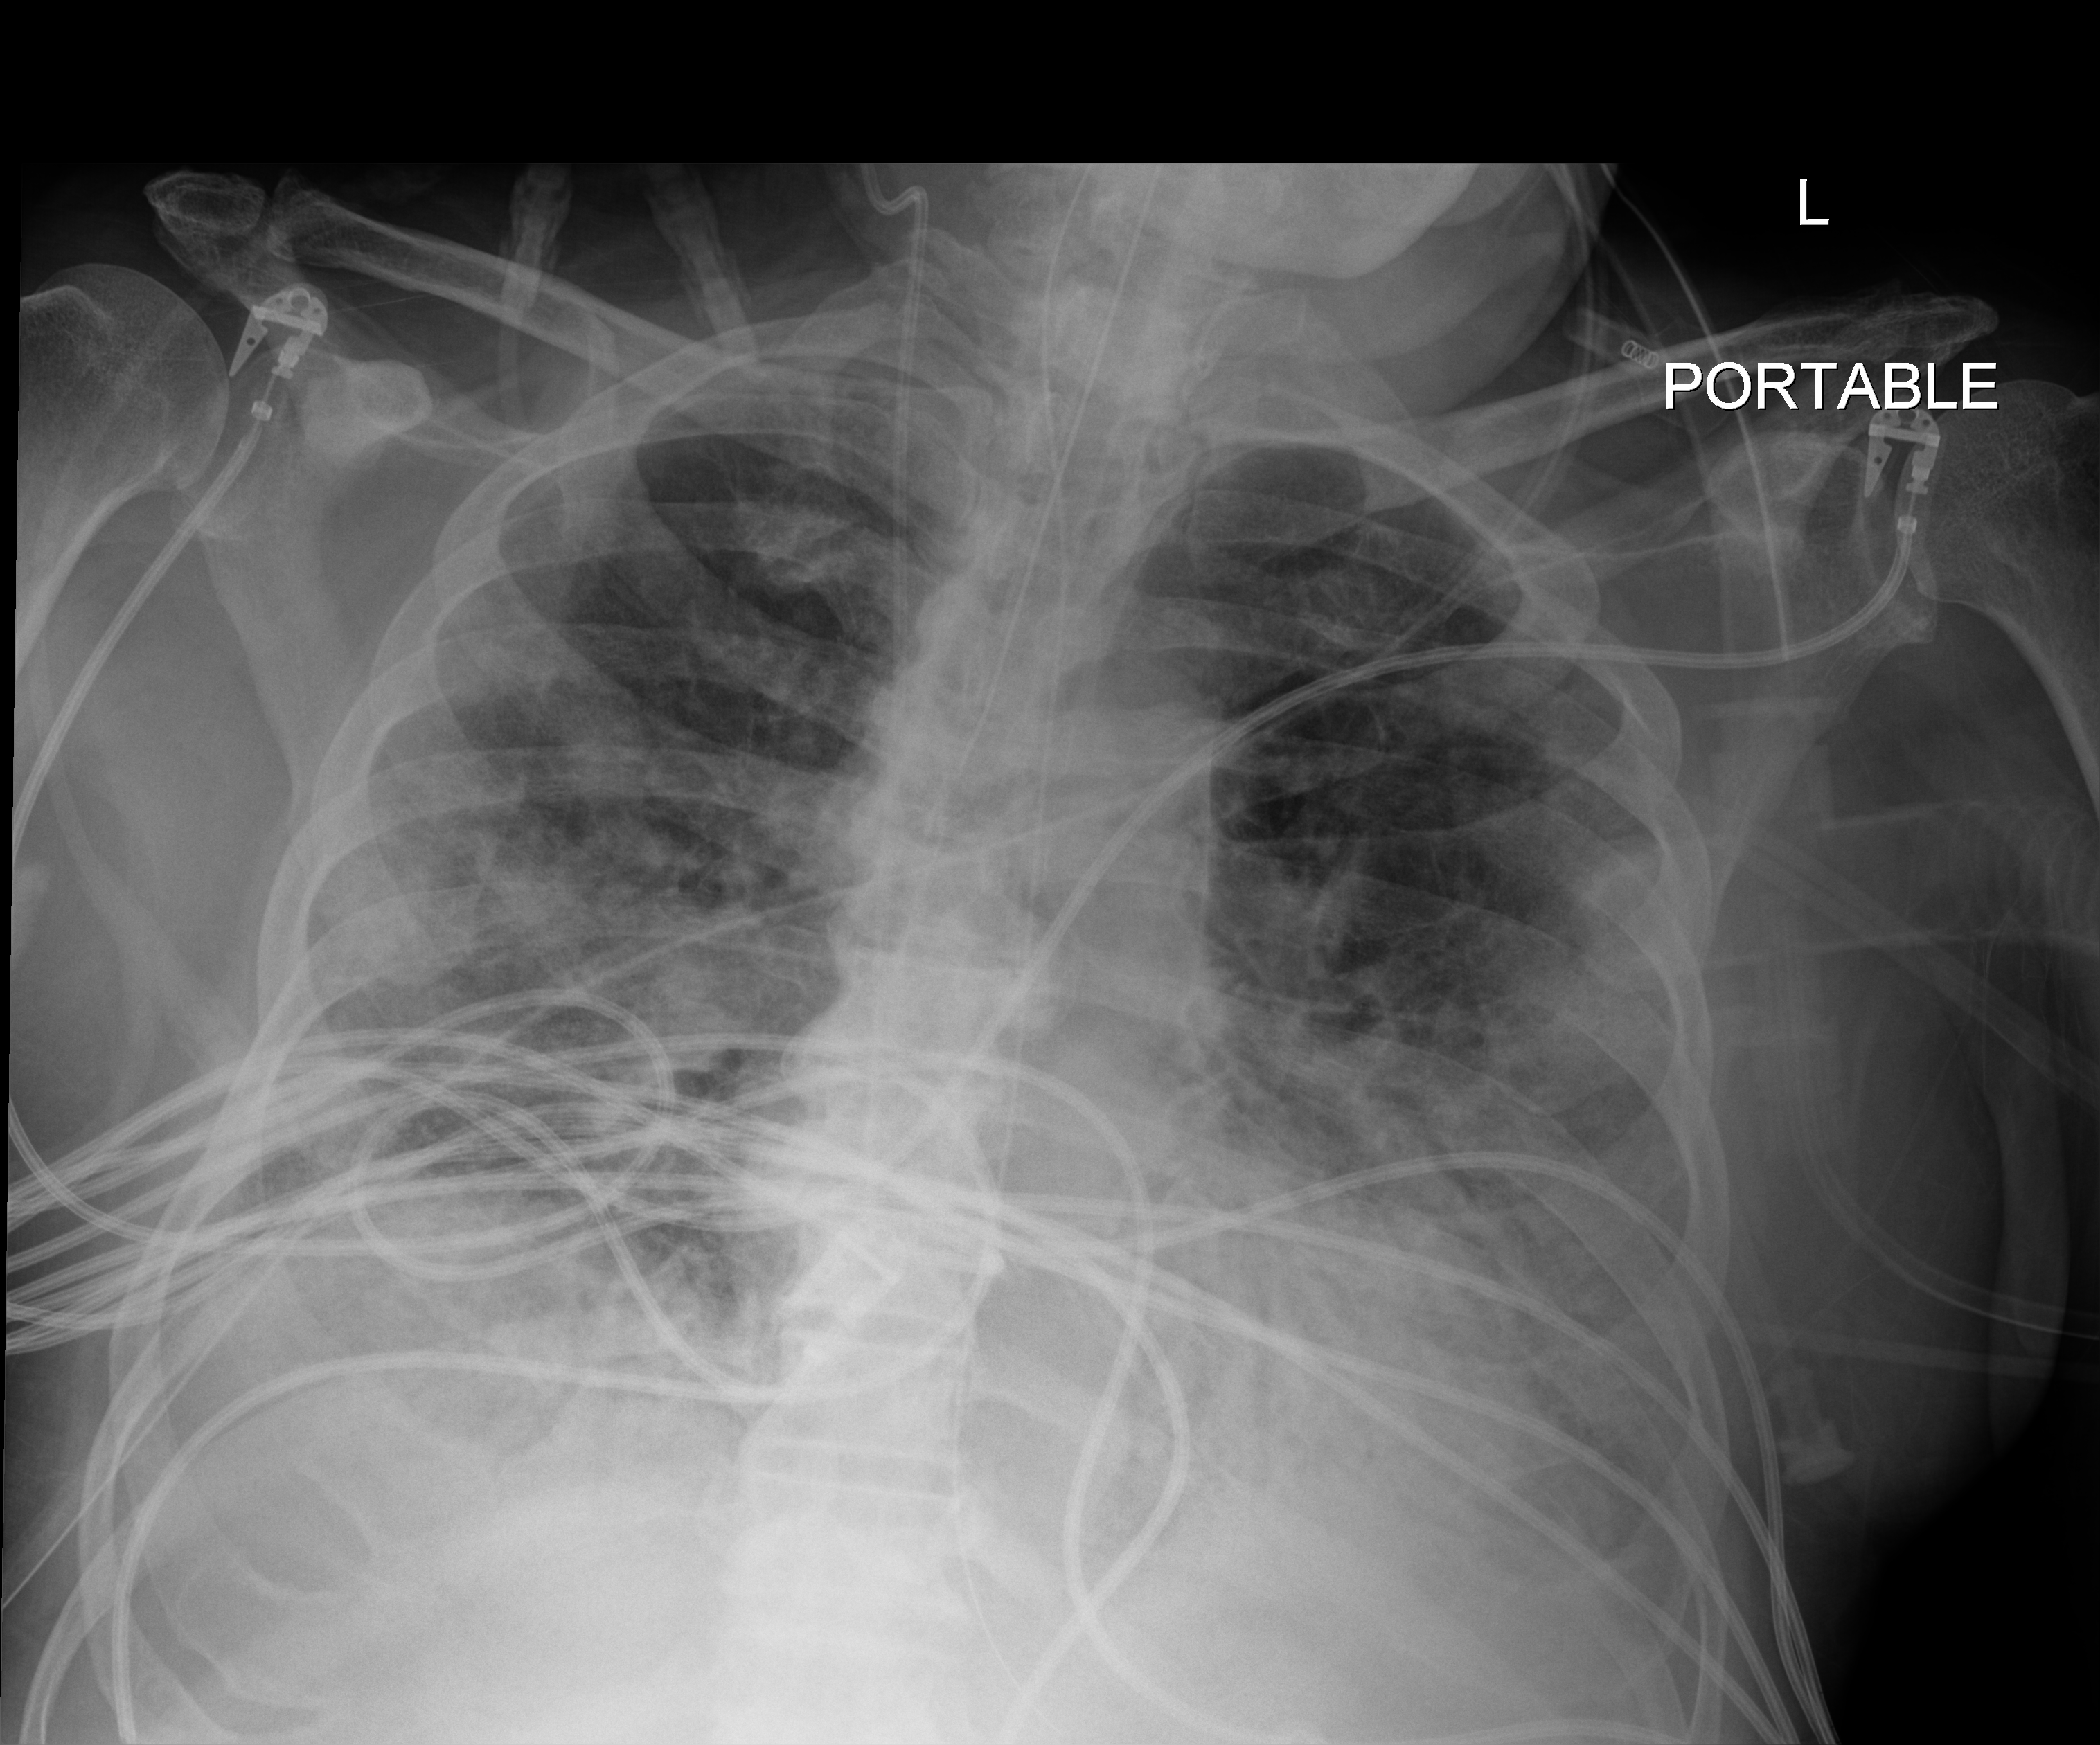
Chest X-ray (portable), anteroposterior (AP) projection. Patient hospitalised with COVID-19; male, aged 75–90 years.
From the hospital-stay record, not from the radiograph (when in the stay this image was taken is not recorded): admitted to intensive care during this hospital stay: yes; COPD (admission record): no; mechanically ventilated during this hospital stay: yes.